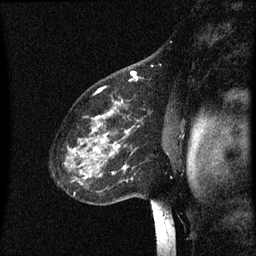
Breast MRI (dynamic contrast-enhanced), one sagittal slice. Slice 46 of 60 in the series (ordered by position). Dynamic contrast-enhanced series, image 2 of 3 at this slice position (ordered by acquisition). 1.5 T. TE 4.2 ms, TR 8 ms. 2 mm slice thickness. 256 × 256 image matrix, field of view 200 × 200 mm. Patient: female, 60 years.
Outlined on this slice (semi-automatically segmented with operator editing):
- analysis volume of interest (the breast-tissue region the enhancement analysis was run in; not a lesion): bounding box <66,98,142,197> (left, top, right, bottom; pixels)
- tumour enhancement mask (voxels above the 70 % enhancement threshold inside the analysis volume of interest): <66,116,128,175>